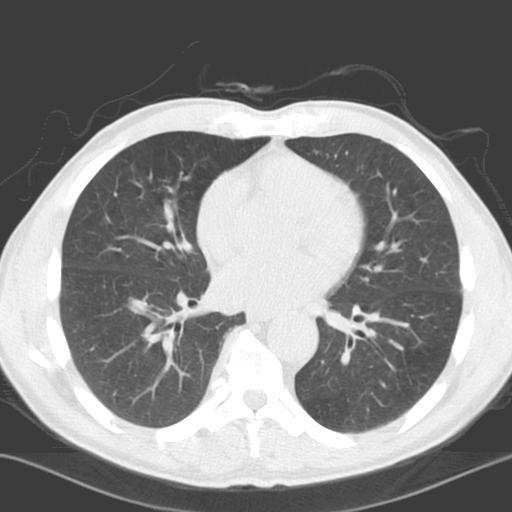
Low-dose screening chest CT, axial slice; baseline annual screen; lung window (W 1500 / L -600 HU); 3.2 mm slice thickness; standard (soft-tissue) reconstruction kernel (C); slice 100 of 178 in the series. Male participant, aged 65 years at enrolment.
Lesion marked by an expert reader, bounding box [x1, y1, x2, y2] px = [135, 165, 200, 229]. Screening reader's record for this exam (one nodule recorded; not confirmed to be the boxed lesion): non-calcified nodule or mass ≥4 mm, right lower lobe, 5 × 5 mm, poorly defined margins, soft tissue attenuation.